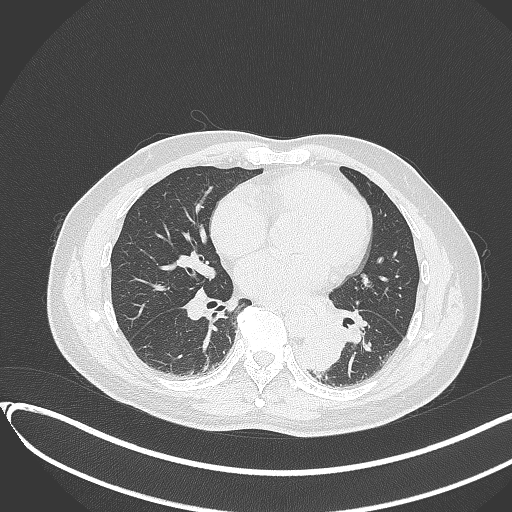
Chest CT, one axial slice. Position 149 of 417 along the scan axis. Reconstruction kernel B70f. 120 kVp. Lung window (W 1500 / L -600 HU). 512 × 512 image matrix, field of view 400 × 400 mm. Male patient, age 54 years. Case-level facts recorded for this patient, not image findings: clinical TNM (as recorded): T3 N0 M0.
Structures marked on this image (rectangle marked by the reading radiologist):
- lung tumour (recorded histology: squamous cell carcinoma): box from (x=291, y=322) to (x=348, y=376) px